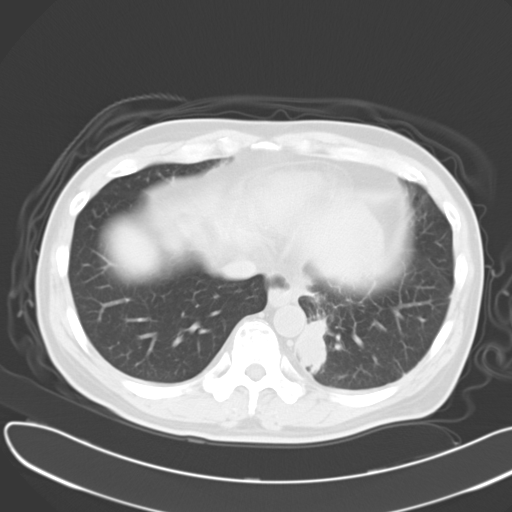
Chest CT, one axial slice; position 9 of 30 along the scan axis; reconstruction kernel B40f; 120 kVp; lung window (W 1500 / L -600 HU); 512 × 512 image matrix, field of view 376 × 376 mm. Patient: male, 55 years. Case-level facts recorded for this patient, not image findings: clinical TNM (as recorded): T2 N3 M0.
Structures marked on this image (bounding box drawn by a radiologist):
- lung tumour (recorded histology: small cell carcinoma): bounding box [x1, y1, x2, y2] px = [298, 321, 337, 377]